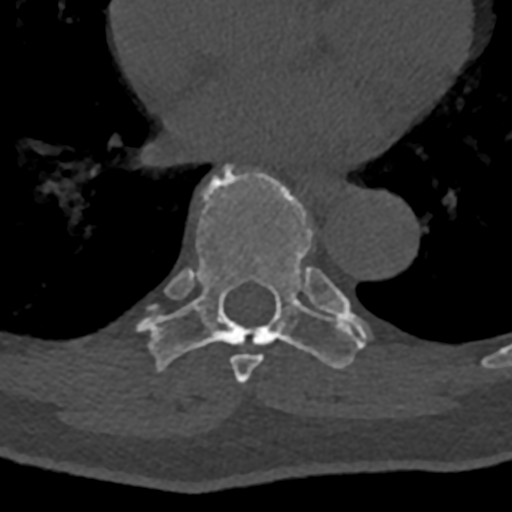
CT including the spine, one axial slice. Position 723 of 797 along the scan axis. 120 kVp. Bone window (W 1800 / L 400 HU). 512 × 512 image matrix, field of view 160 × 160 mm. Male patient, age 74 years. Case-level facts recorded for this patient, not image findings: primary cancer: renal.
Structures marked on this image (semi-automatically segmented with operator editing):
- T7 vertebra: bounding box (x1, y1, x2, y2) in pixels: (230, 270, 344, 384)
- T8 vertebra: (138, 163, 369, 369)